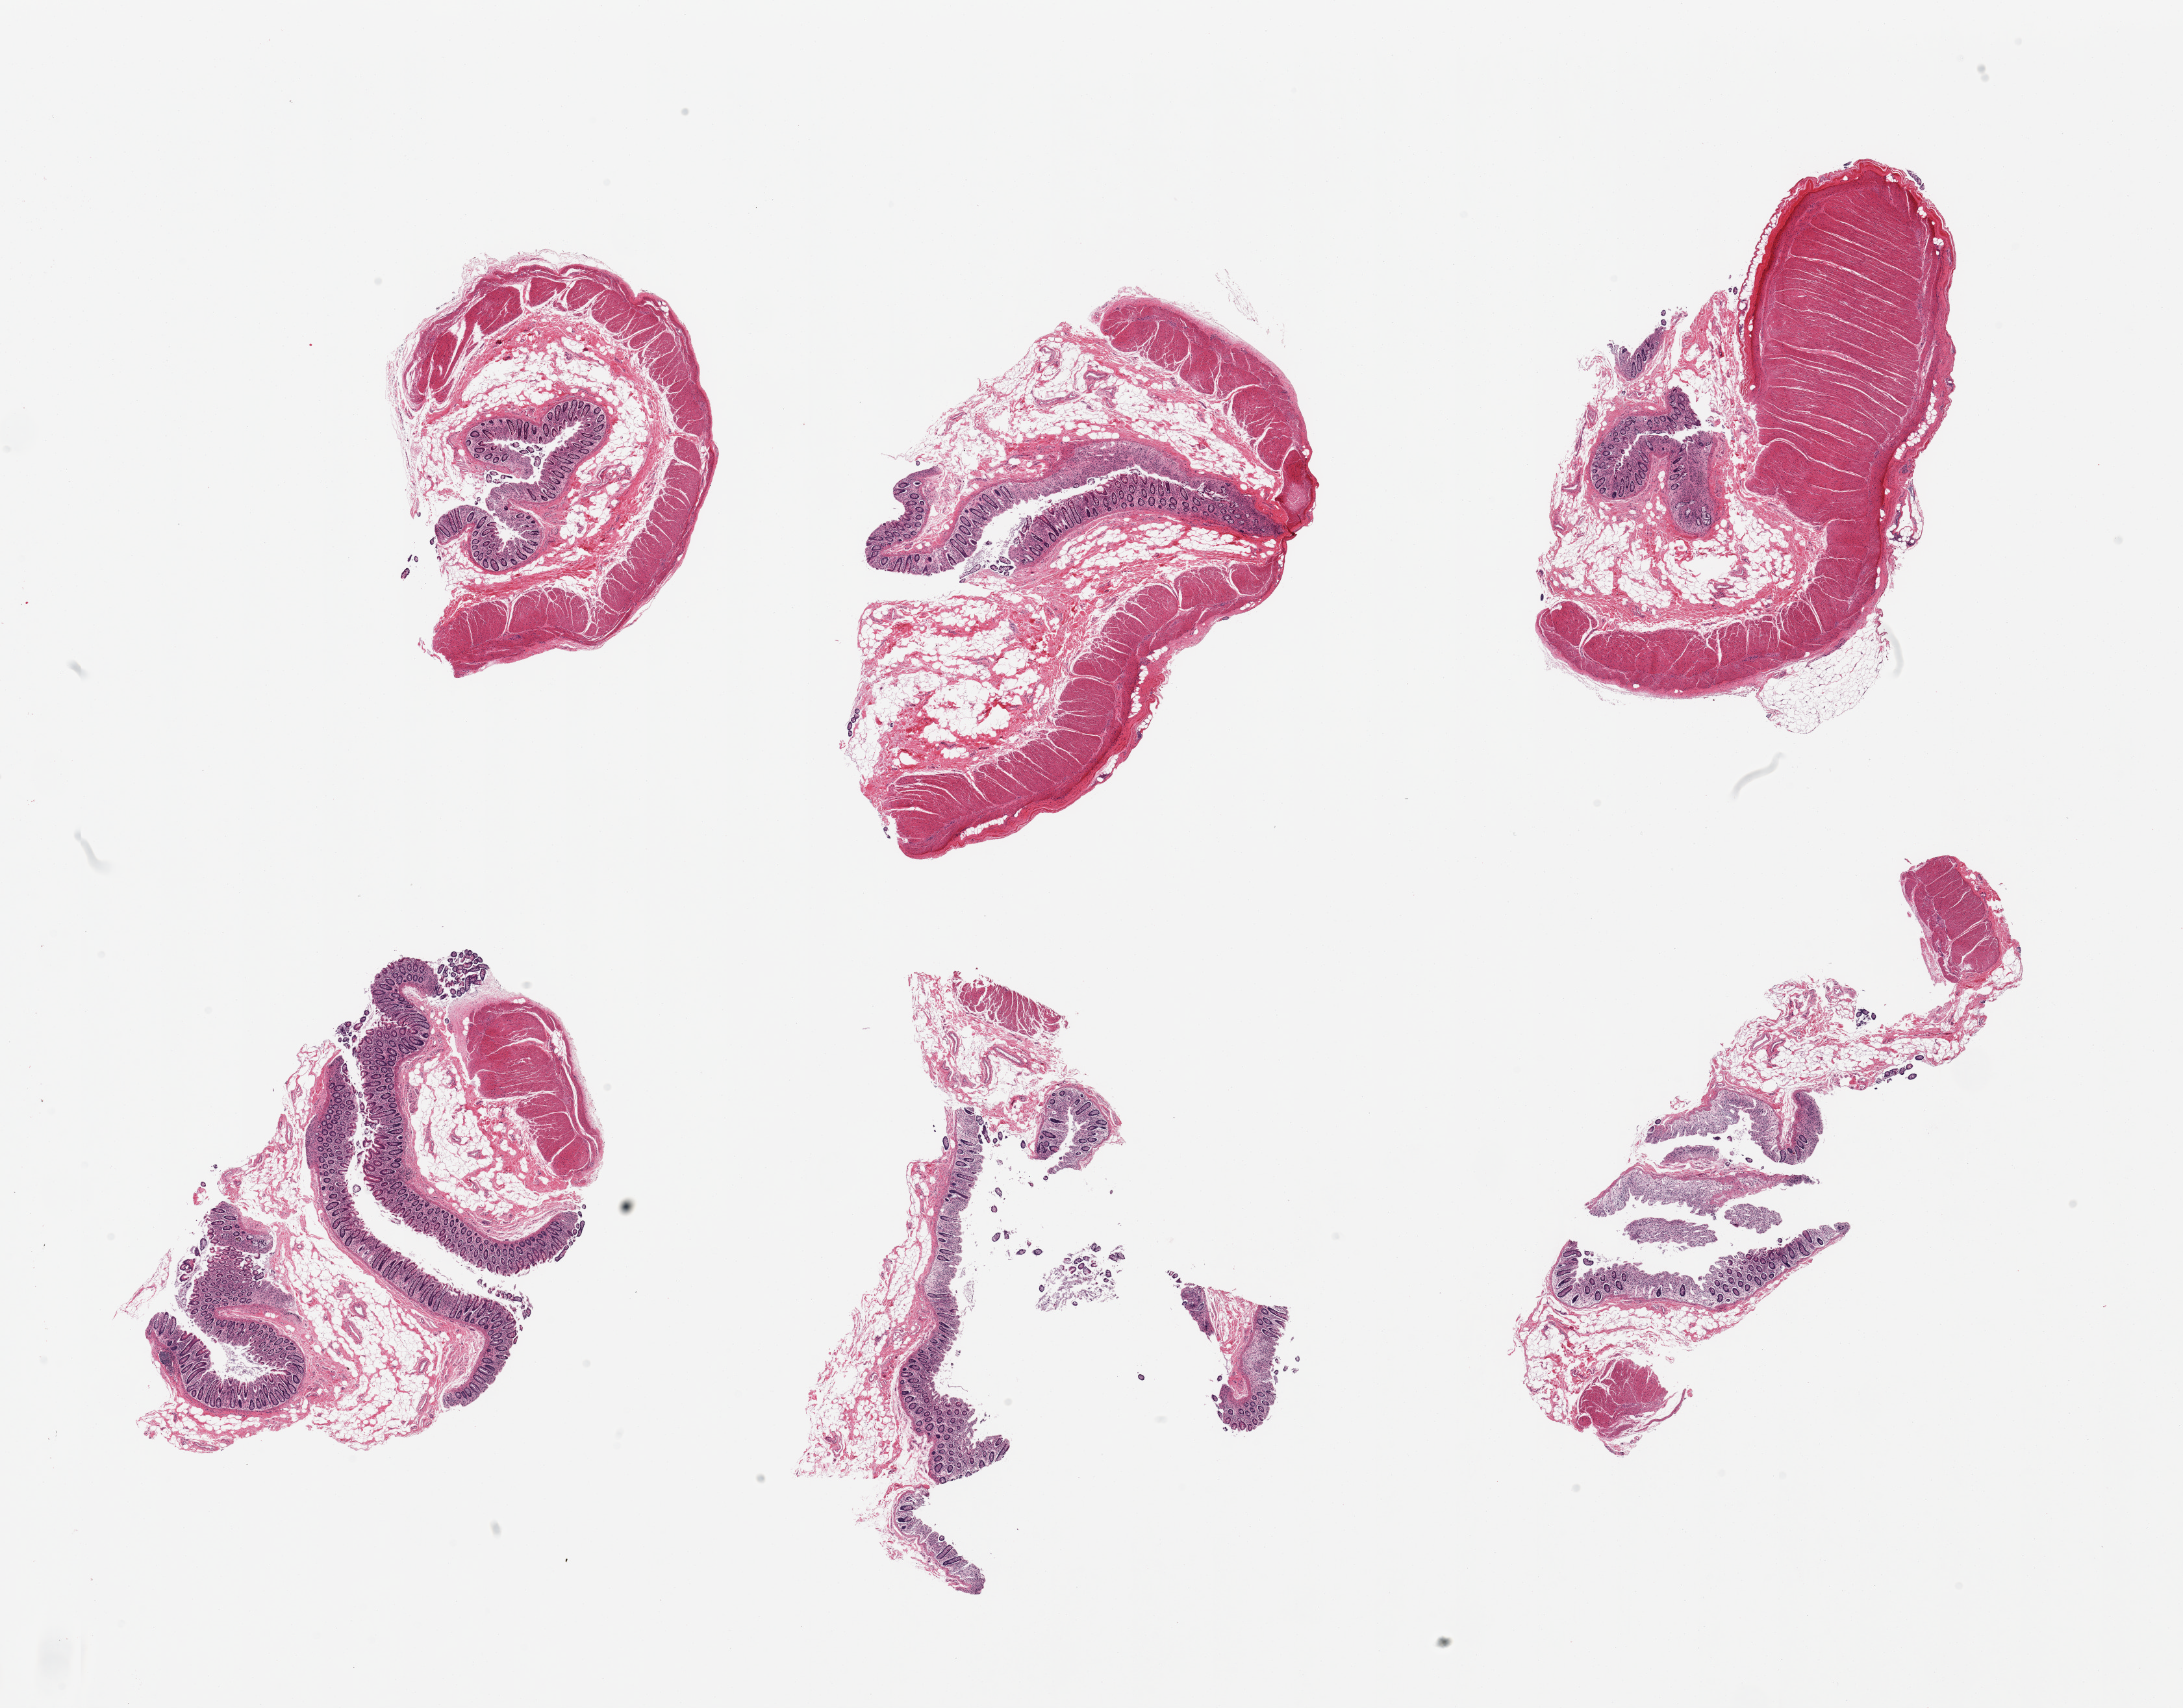
Whole-slide image, H&E stain, whole scanned area (about 26.6 x 20.8 mm) shown as a low-resolution overview, PAXgene-fixed, paraffin-embedded tissue, section of transverse colon (target tissue), tissue donor sample. Donor sex: female.
Reviewer comment on this tissue sample: 6 pieces, mucosa layer up to ~0.4mm variably but generally poorly preserved/sloughing.